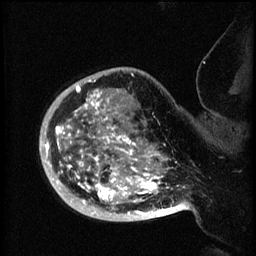
Breast MRI (dynamic contrast-enhanced), one sagittal slice. Position 50 of 60 along the scan axis. 3 images stored at this slice position (order not interpretable as contrast timing). 1.5 T. TE 4.2 ms, TR 8.2 ms. 2 mm slice thickness. 256 × 256 image matrix. Patient: female, 50 years.
Structures marked on this image (semi-automatic segmentation, software-assisted and operator-edited):
- analysis volume of interest (the breast-tissue region the enhancement analysis was run in; not a lesion): bounding box [x1, y1, x2, y2] px = [44, 72, 173, 219]
- tumour enhancement mask (voxels above the 70 % enhancement threshold inside the analysis volume of interest): [45, 80, 173, 217]